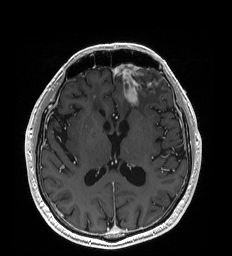
Brain MRI from a brain-tumour surgery series, one axial slice. Slice 99 of 192 in the series (ordered by position). T1-weighted post-contrast. 1 mm slice thickness. 232 × 256 image matrix. Case-level facts recorded for this patient, not image findings: histopathology: Glioblastoma; WHO grade: 4; IDH mutation: no.
Structures marked on this image (manually delineated by an expert):
- tumour: bounding box <125,88,138,105> (left, top, right, bottom; pixels)